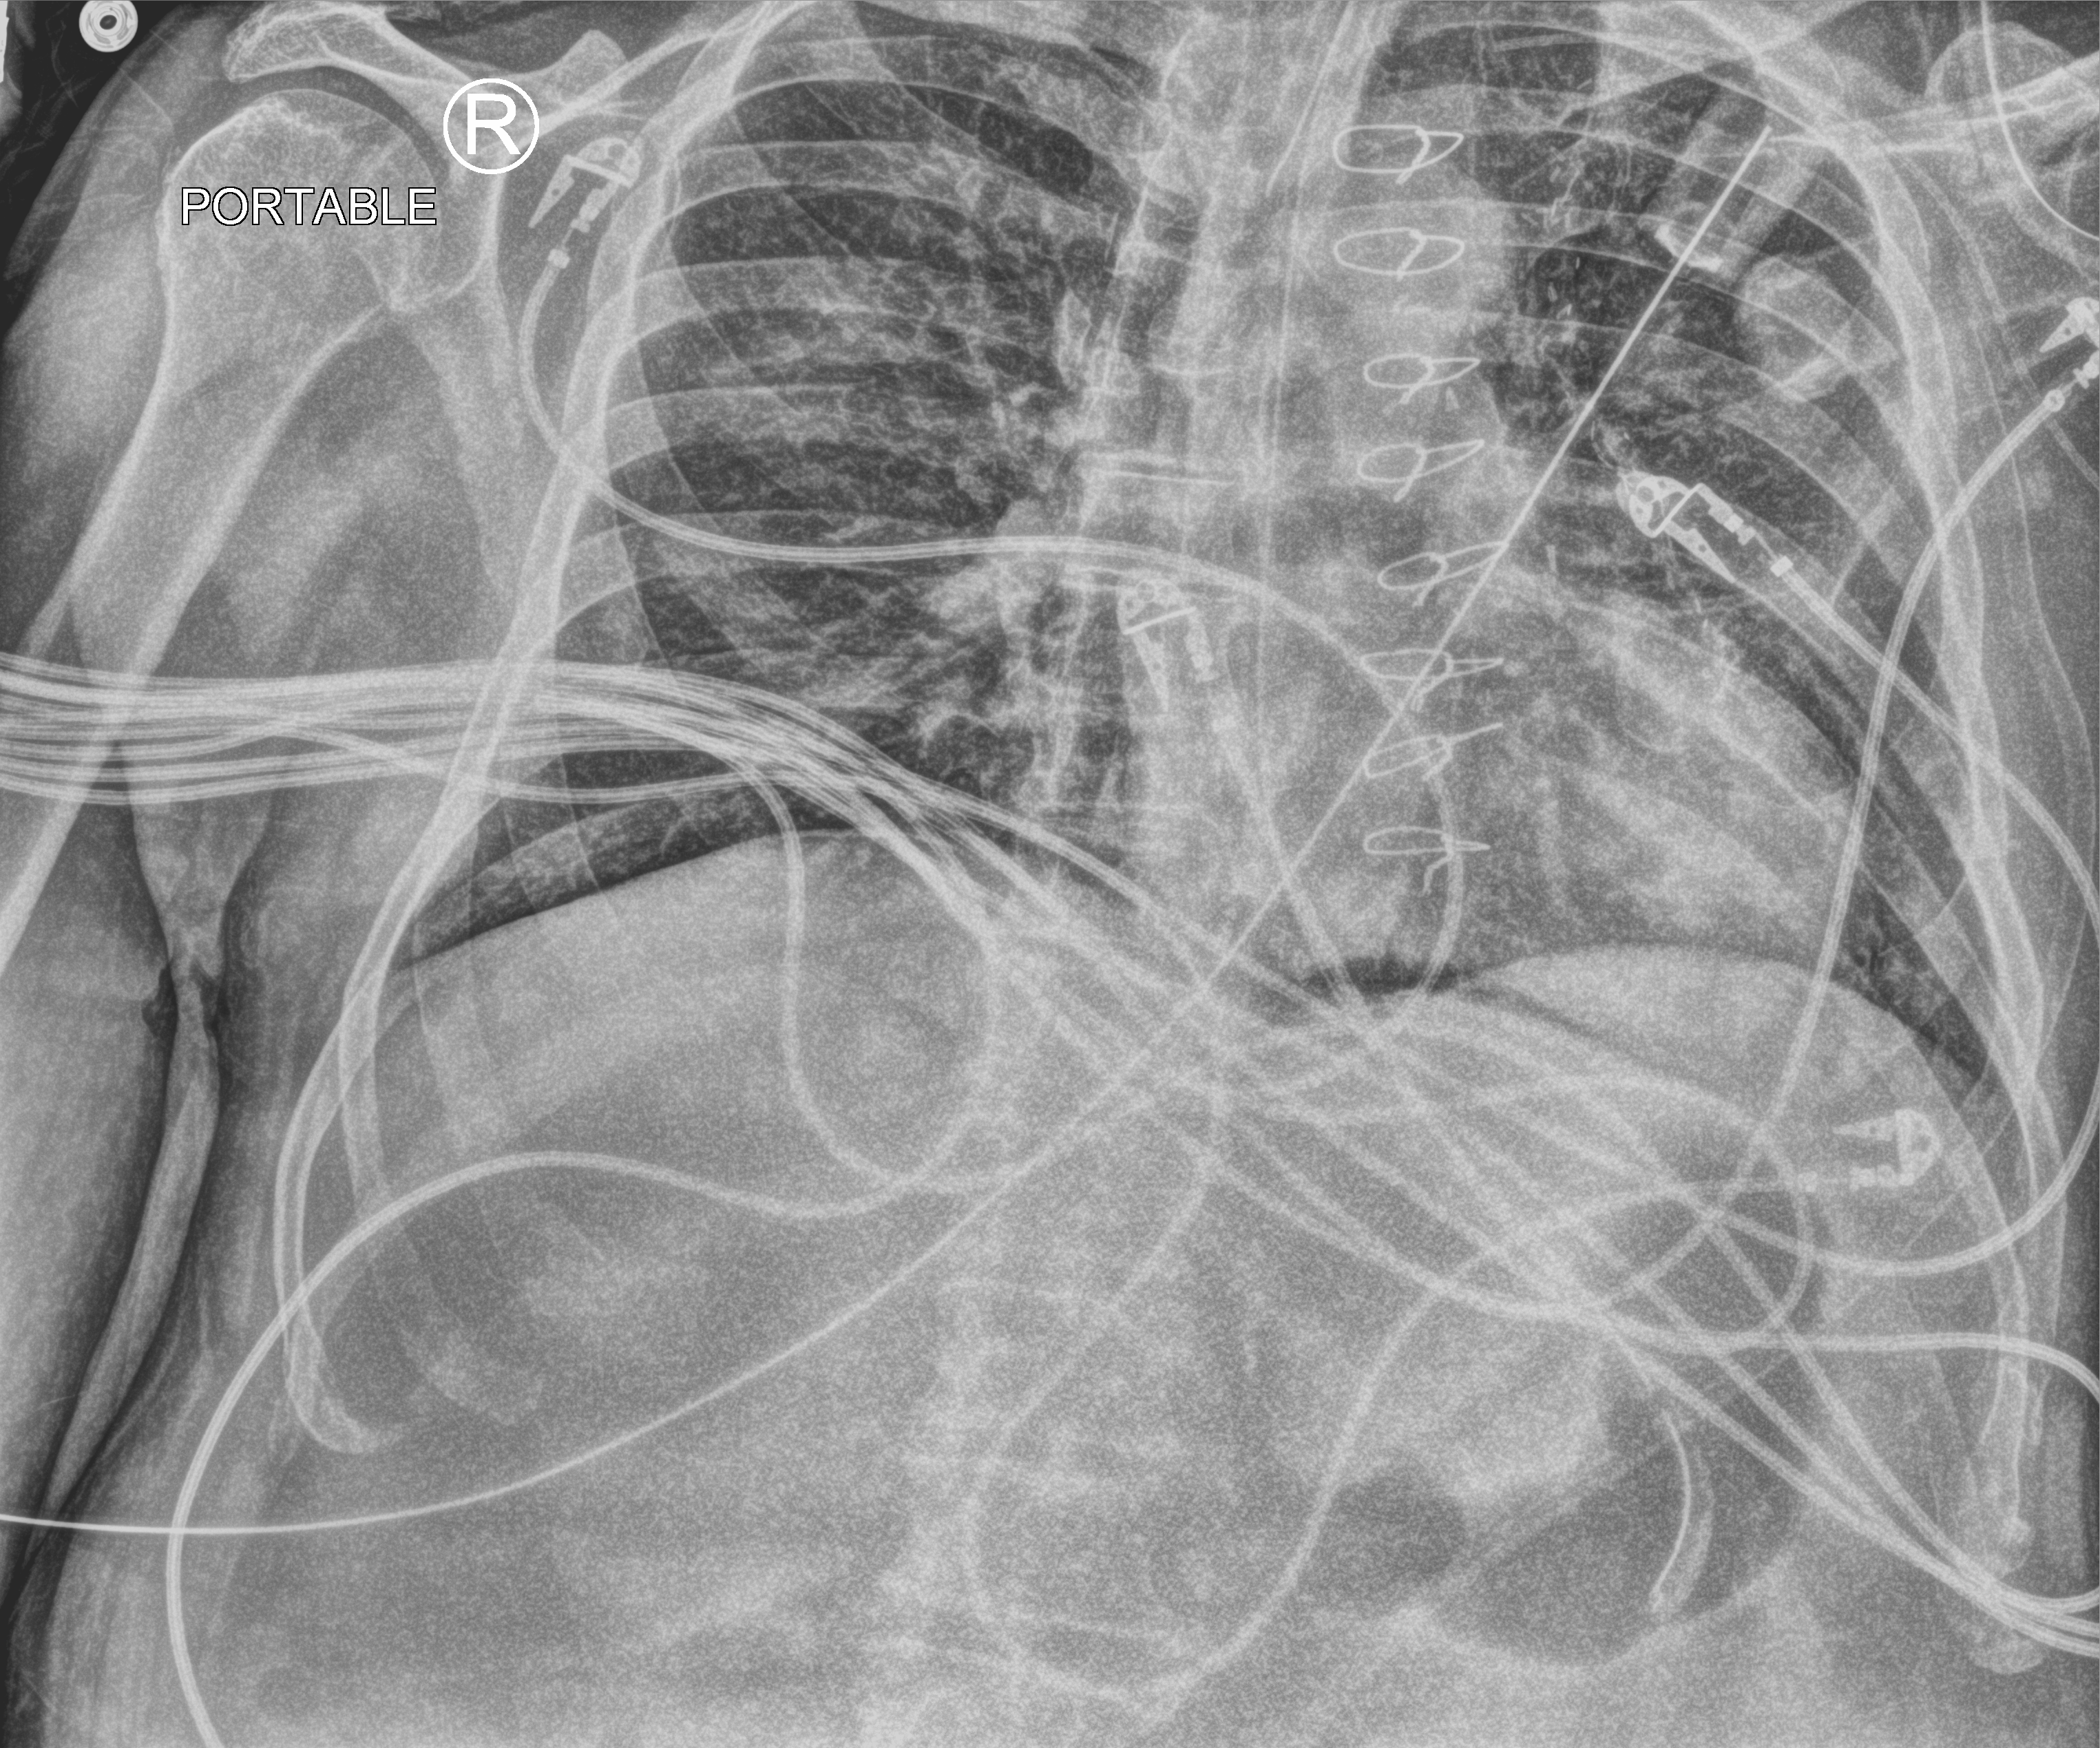
Portable chest radiograph, anteroposterior (AP) projection. Male patient hospitalised with COVID-19, age 60–74 years.
From the hospital-stay record, not from the radiograph (when in the stay this image was taken is not recorded): smoking status (admission record): never.